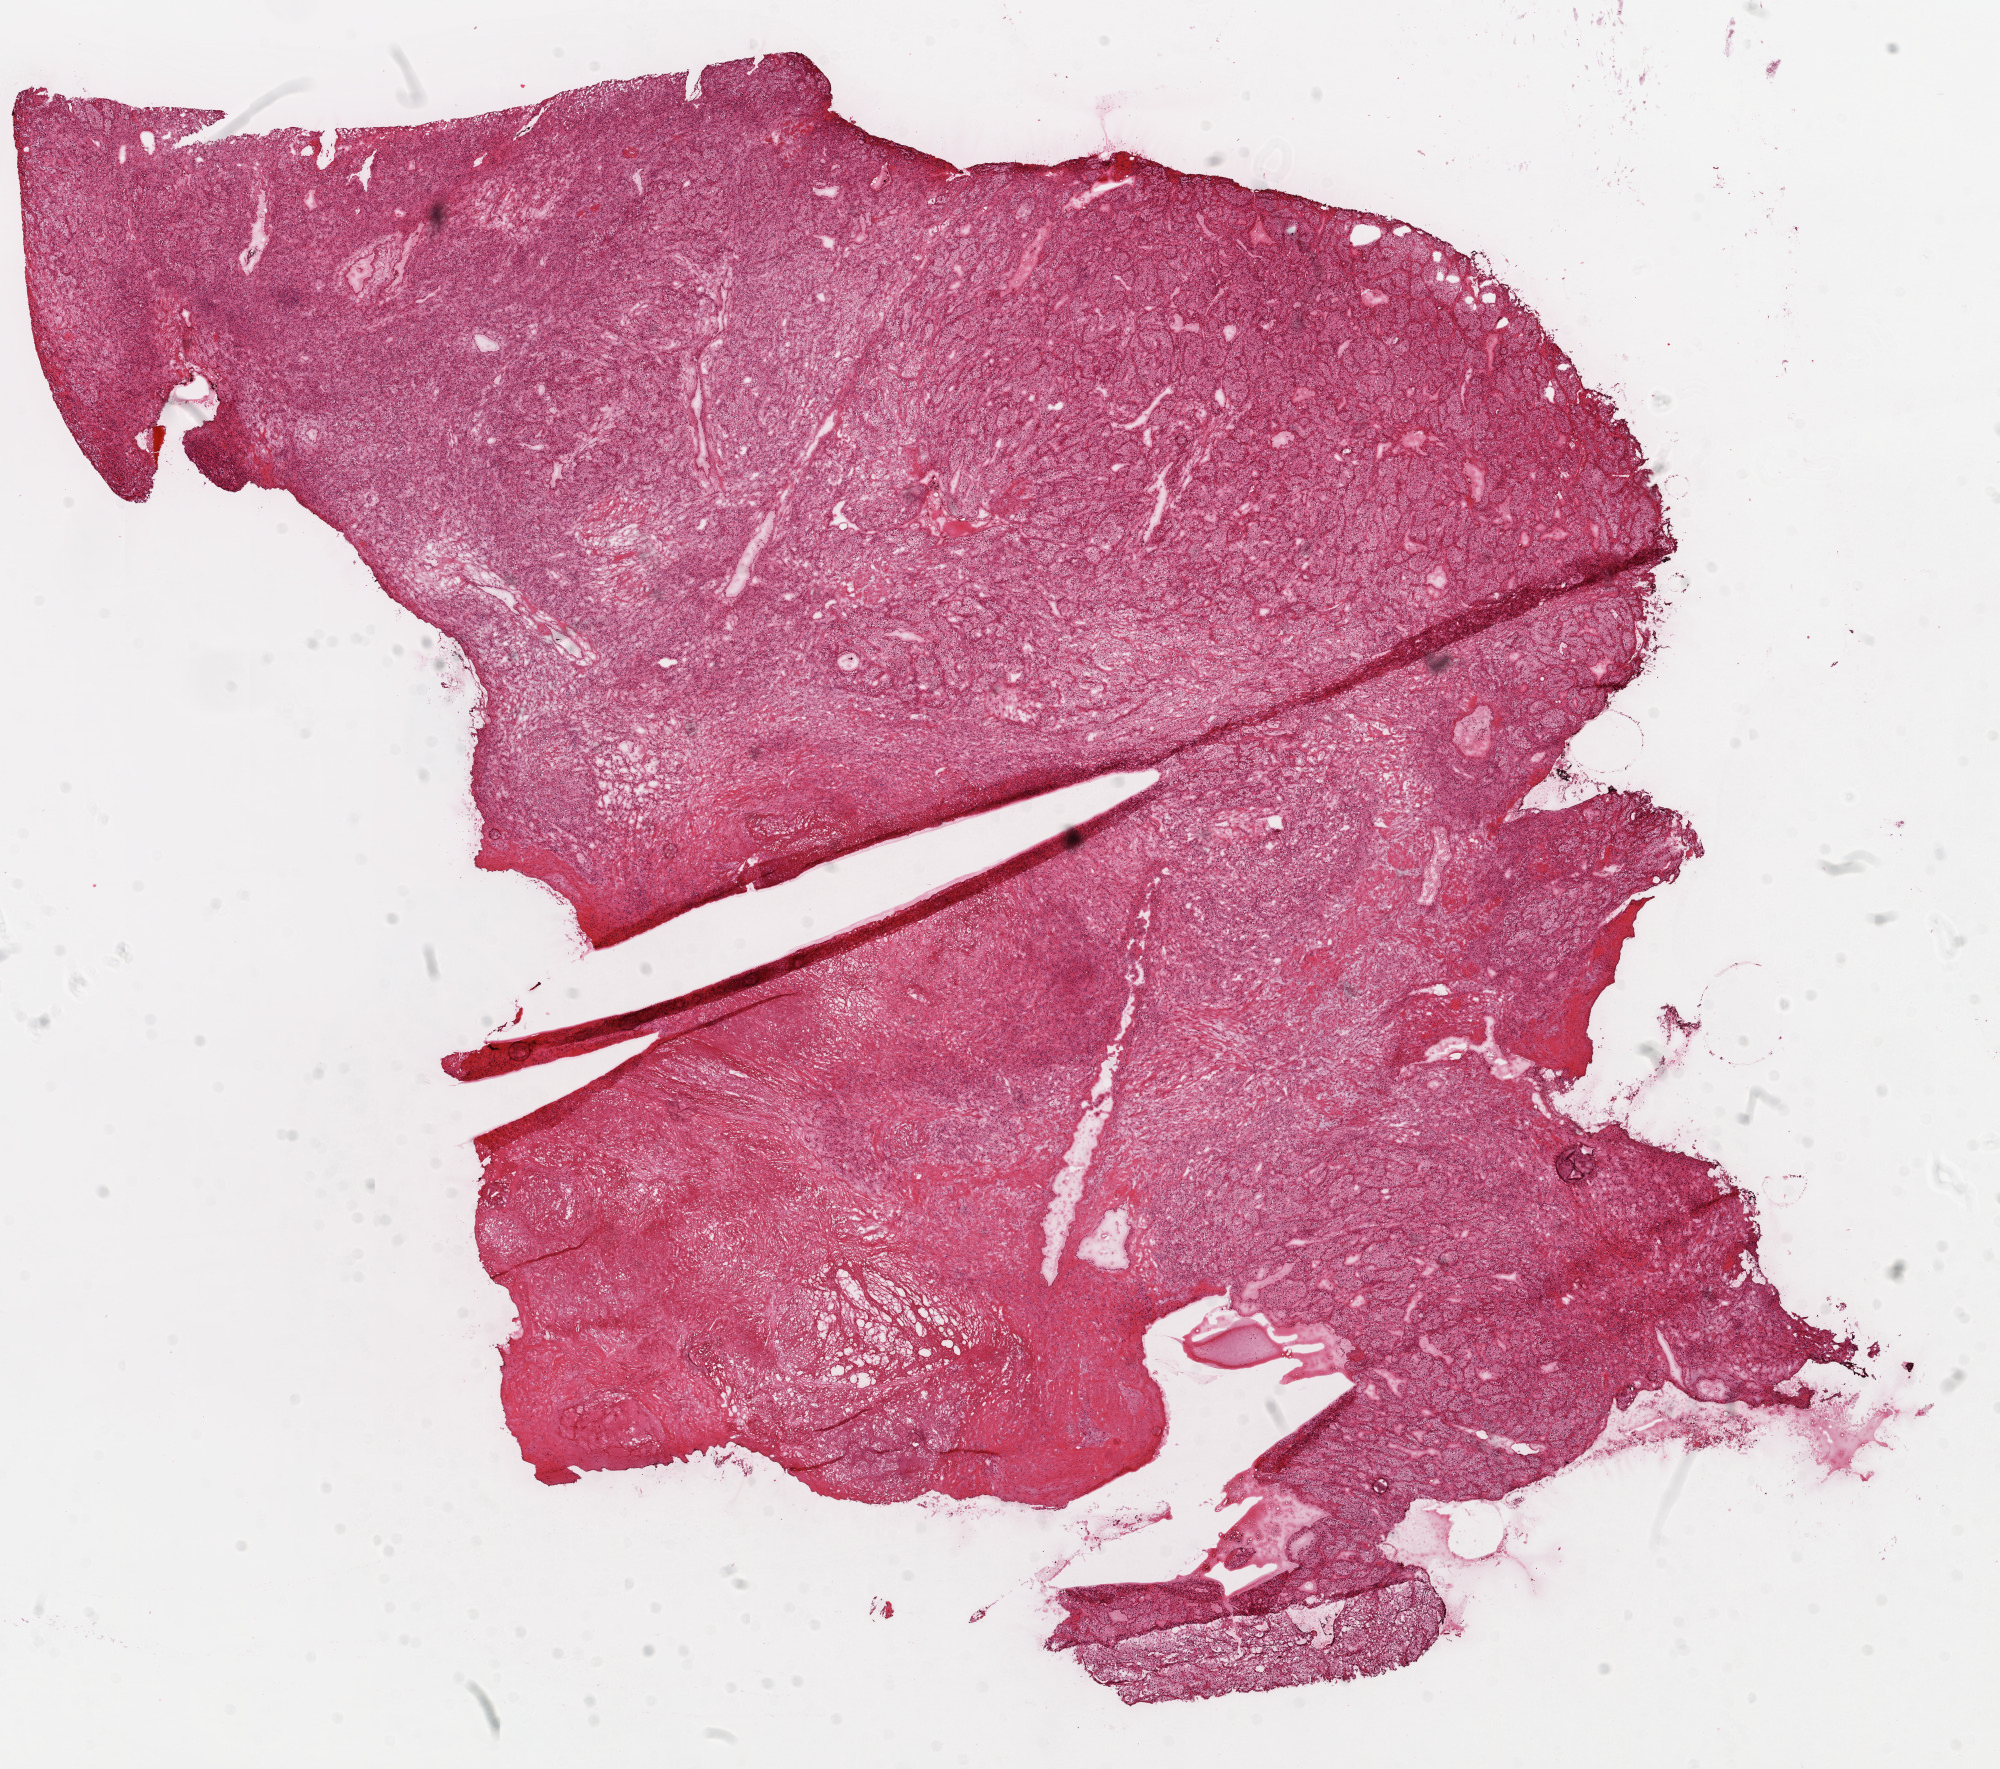
Digitized H&E tissue section (whole slide) — whole scanned area (about 16.0 x 14.2 mm, acquisition: 20x scan) shown as a low-resolution overview; frozen section from the top of the tissue portion; primary tumour sample from the kidney. Male patient; age at initial diagnosis 62 years. Histologic grade: G3 (poorly differentiated). Composition of this section per pathologist review: tumour cells 85%, tumour nuclei 80%, normal cells 0%, stromal cells 15%, necrosis 0%.
- diagnosis: Clear cell adenocarcinoma, NOS
- lymph nodes positive (case pathology): 0 of 1 examined
- AJCC pathologic stage: III
- TNM: T3b N0 M0